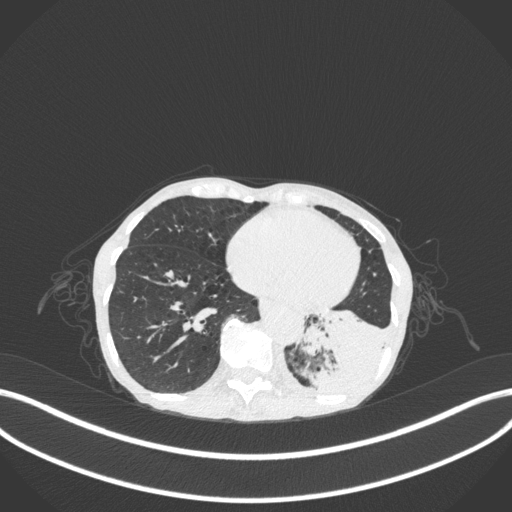
Chest CT, one axial slice. Position 72 of 347 along the scan axis. 120 kVp. Lung window (W 1500 / L -600 HU). 512 × 512 image matrix, field of view 400 × 400 mm. Patient: female, 70 years. From the clinical record (not read from this slice): clinical TNM (as recorded): T3 N0 M0.
Annotated regions visible in this slice (rectangle marked by the reading radiologist):
- lung tumour (recorded histology: small cell carcinoma): bounding box (x1, y1, x2, y2) in pixels: (298, 303, 382, 404)